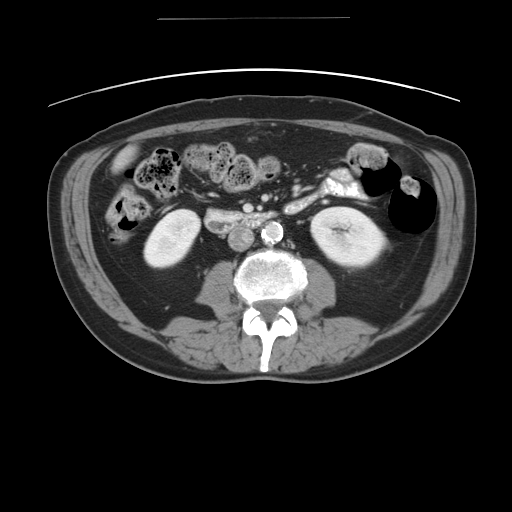
Contrast-enhanced abdominal CT, one axial slice. Position 10 of 49 along the scan axis. Reconstruction kernel STANDARD. Soft-tissue window (W 400 / L 40 HU). 5 mm slice thickness. 512 × 512 image matrix, field of view 413 × 413 mm. Male patient, age 57 years. From the clinical record (not read from this slice): diagnosis: colorectal cancer liver metastases, imaged before liver resection; multiple liver metastases: yes.
Structures marked on this image (expert manual segmentation):
- liver: box from (x=118, y=153) to (x=127, y=165) px